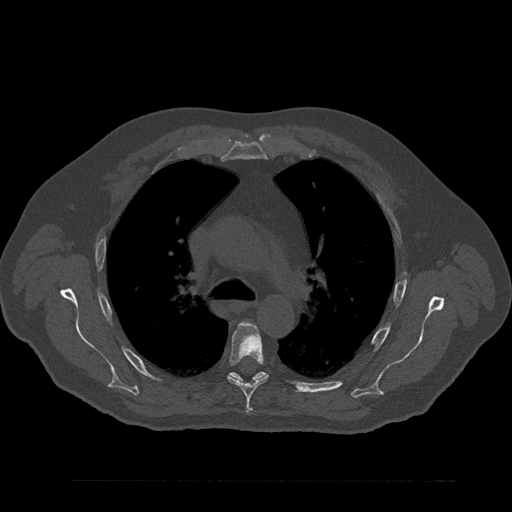
CT including the spine, one axial slice. Slice 594 of 797 in the series (ordered by position). Reconstruction kernel Br40s/3. 120 kVp. Bone window (W 1800 / L 400 HU). 512 × 512 image matrix, field of view 430 × 430 mm. Patient: male, 61 years. From the clinical record (not read from this slice): primary cancer: prostate.
Annotated regions visible in this slice (semi-automatic segmentation, software-assisted and operator-edited):
- T5 vertebra: bounding box <227,322,268,411> (left, top, right, bottom; pixels)
- T6 vertebra: <228,365,267,382>